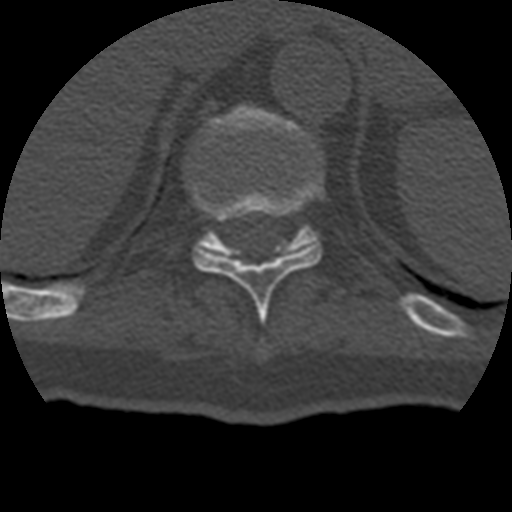
CT including the spine, one axial slice. Reconstruction kernel STANDARD. 120 kVp. Bone window (W 1800 / L 400 HU). 1.25 mm slice thickness. 512 × 512 image matrix, field of view 160 × 160 mm. Patient age 69 years. From the clinical record (not read from this slice): primary cancer: prostate.
Outlined on this slice (semi-automatically segmented with operator editing):
- T10 vertebra: bounding box <194,186,322,319> (left, top, right, bottom; pixels)
- T11 vertebra: <199,105,319,251>